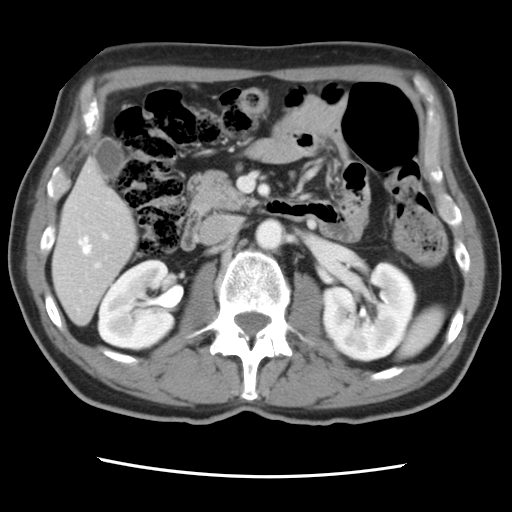
Contrast-enhanced abdominal CT, one axial slice; 120 kVp; intravenous contrast given; soft-tissue window (W 400 / L 40 HU); 5 mm slice thickness; 512 × 512 image matrix. Male patient, age 69 years. From the clinical record (not read from this slice): diagnosis: colorectal cancer liver metastases, imaged before liver resection; multiple liver metastases: yes; largest metastasis: 3.5 cm; disease in both lobes: no.
Structures marked on this image (manually delineated by an expert):
- hepatic veins: bounding box (x1, y1, x2, y2) in pixels: (78, 236, 92, 255)
- liver: (53, 163, 137, 323)
- planned liver remnant (the part of the liver to remain after resection): (53, 164, 137, 324)
- portal vein (with intrahepatic branches): (79, 232, 109, 293)